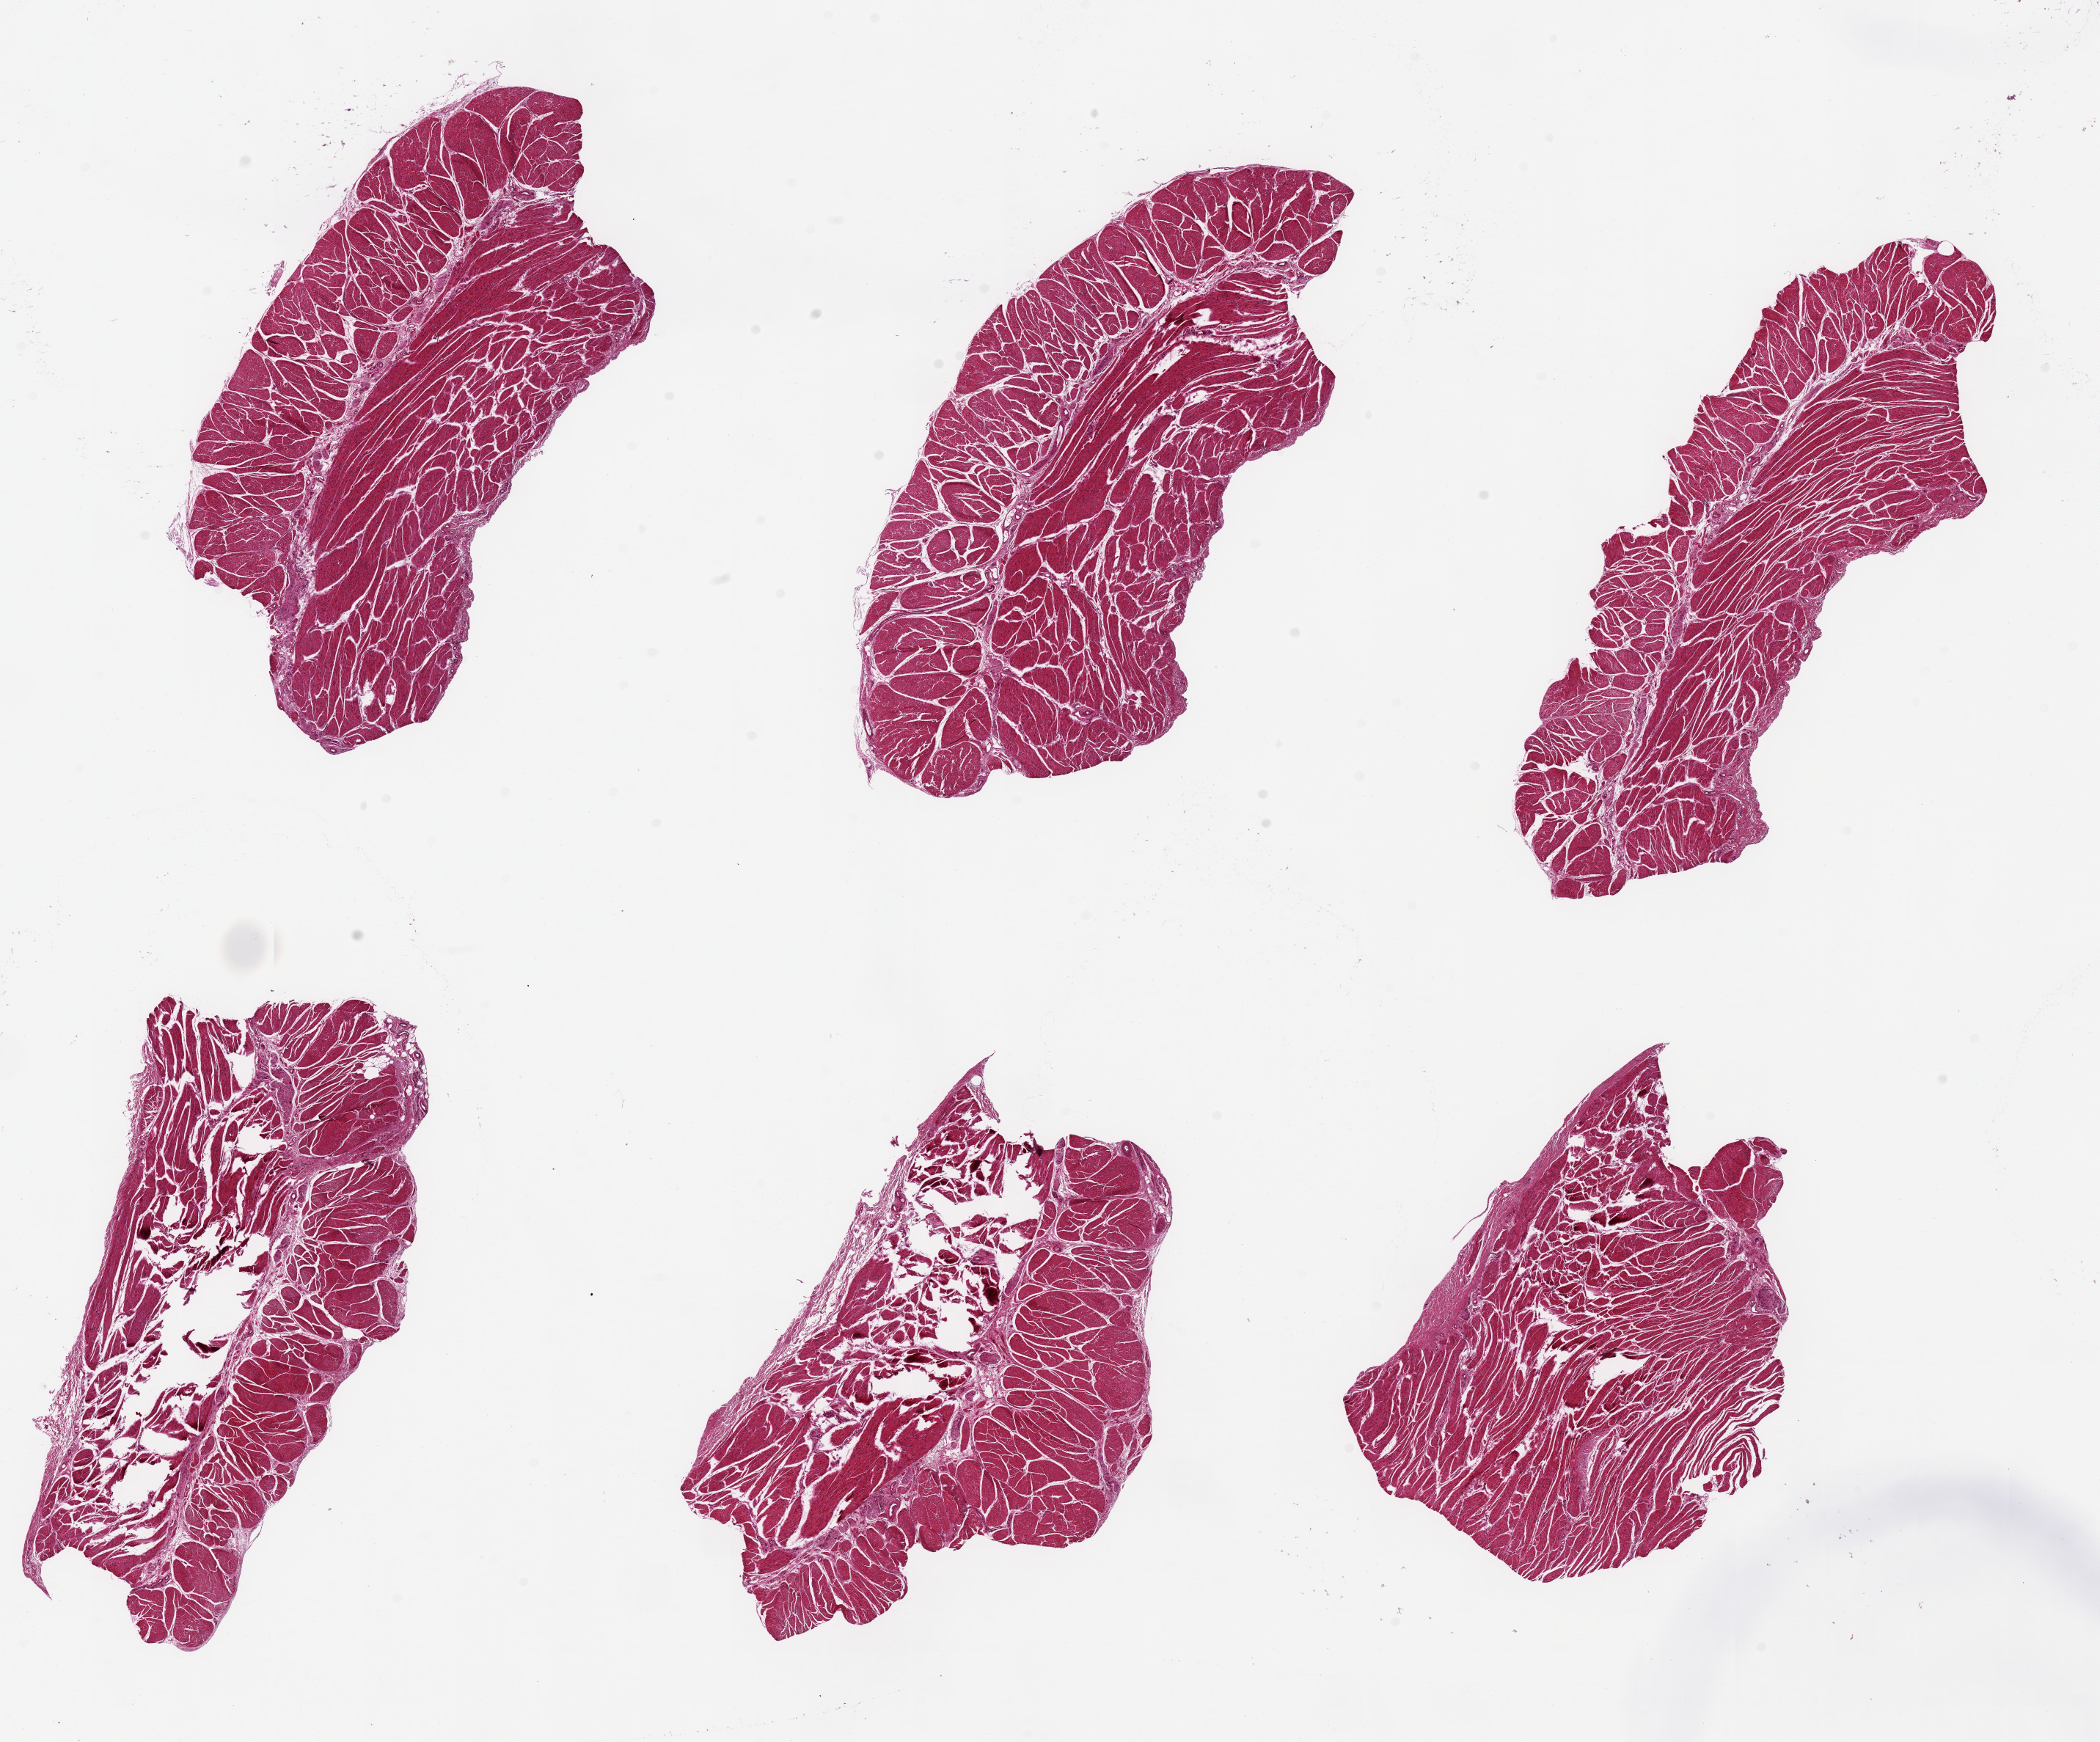
Hematoxylin and eosin (H&E) whole-slide image — a low-resolution overview of the entire scanned area, about 22.6 x 18.8 mm (acquisition: 20x scan), PAXgene-fixed, paraffin-embedded tissue, sampled site (target tissue): esophageal muscle, tissue donor sample.
Pathologist's review note for this sample: 6 pieces, up to 8x3mm; good pure muscularis propria in all.